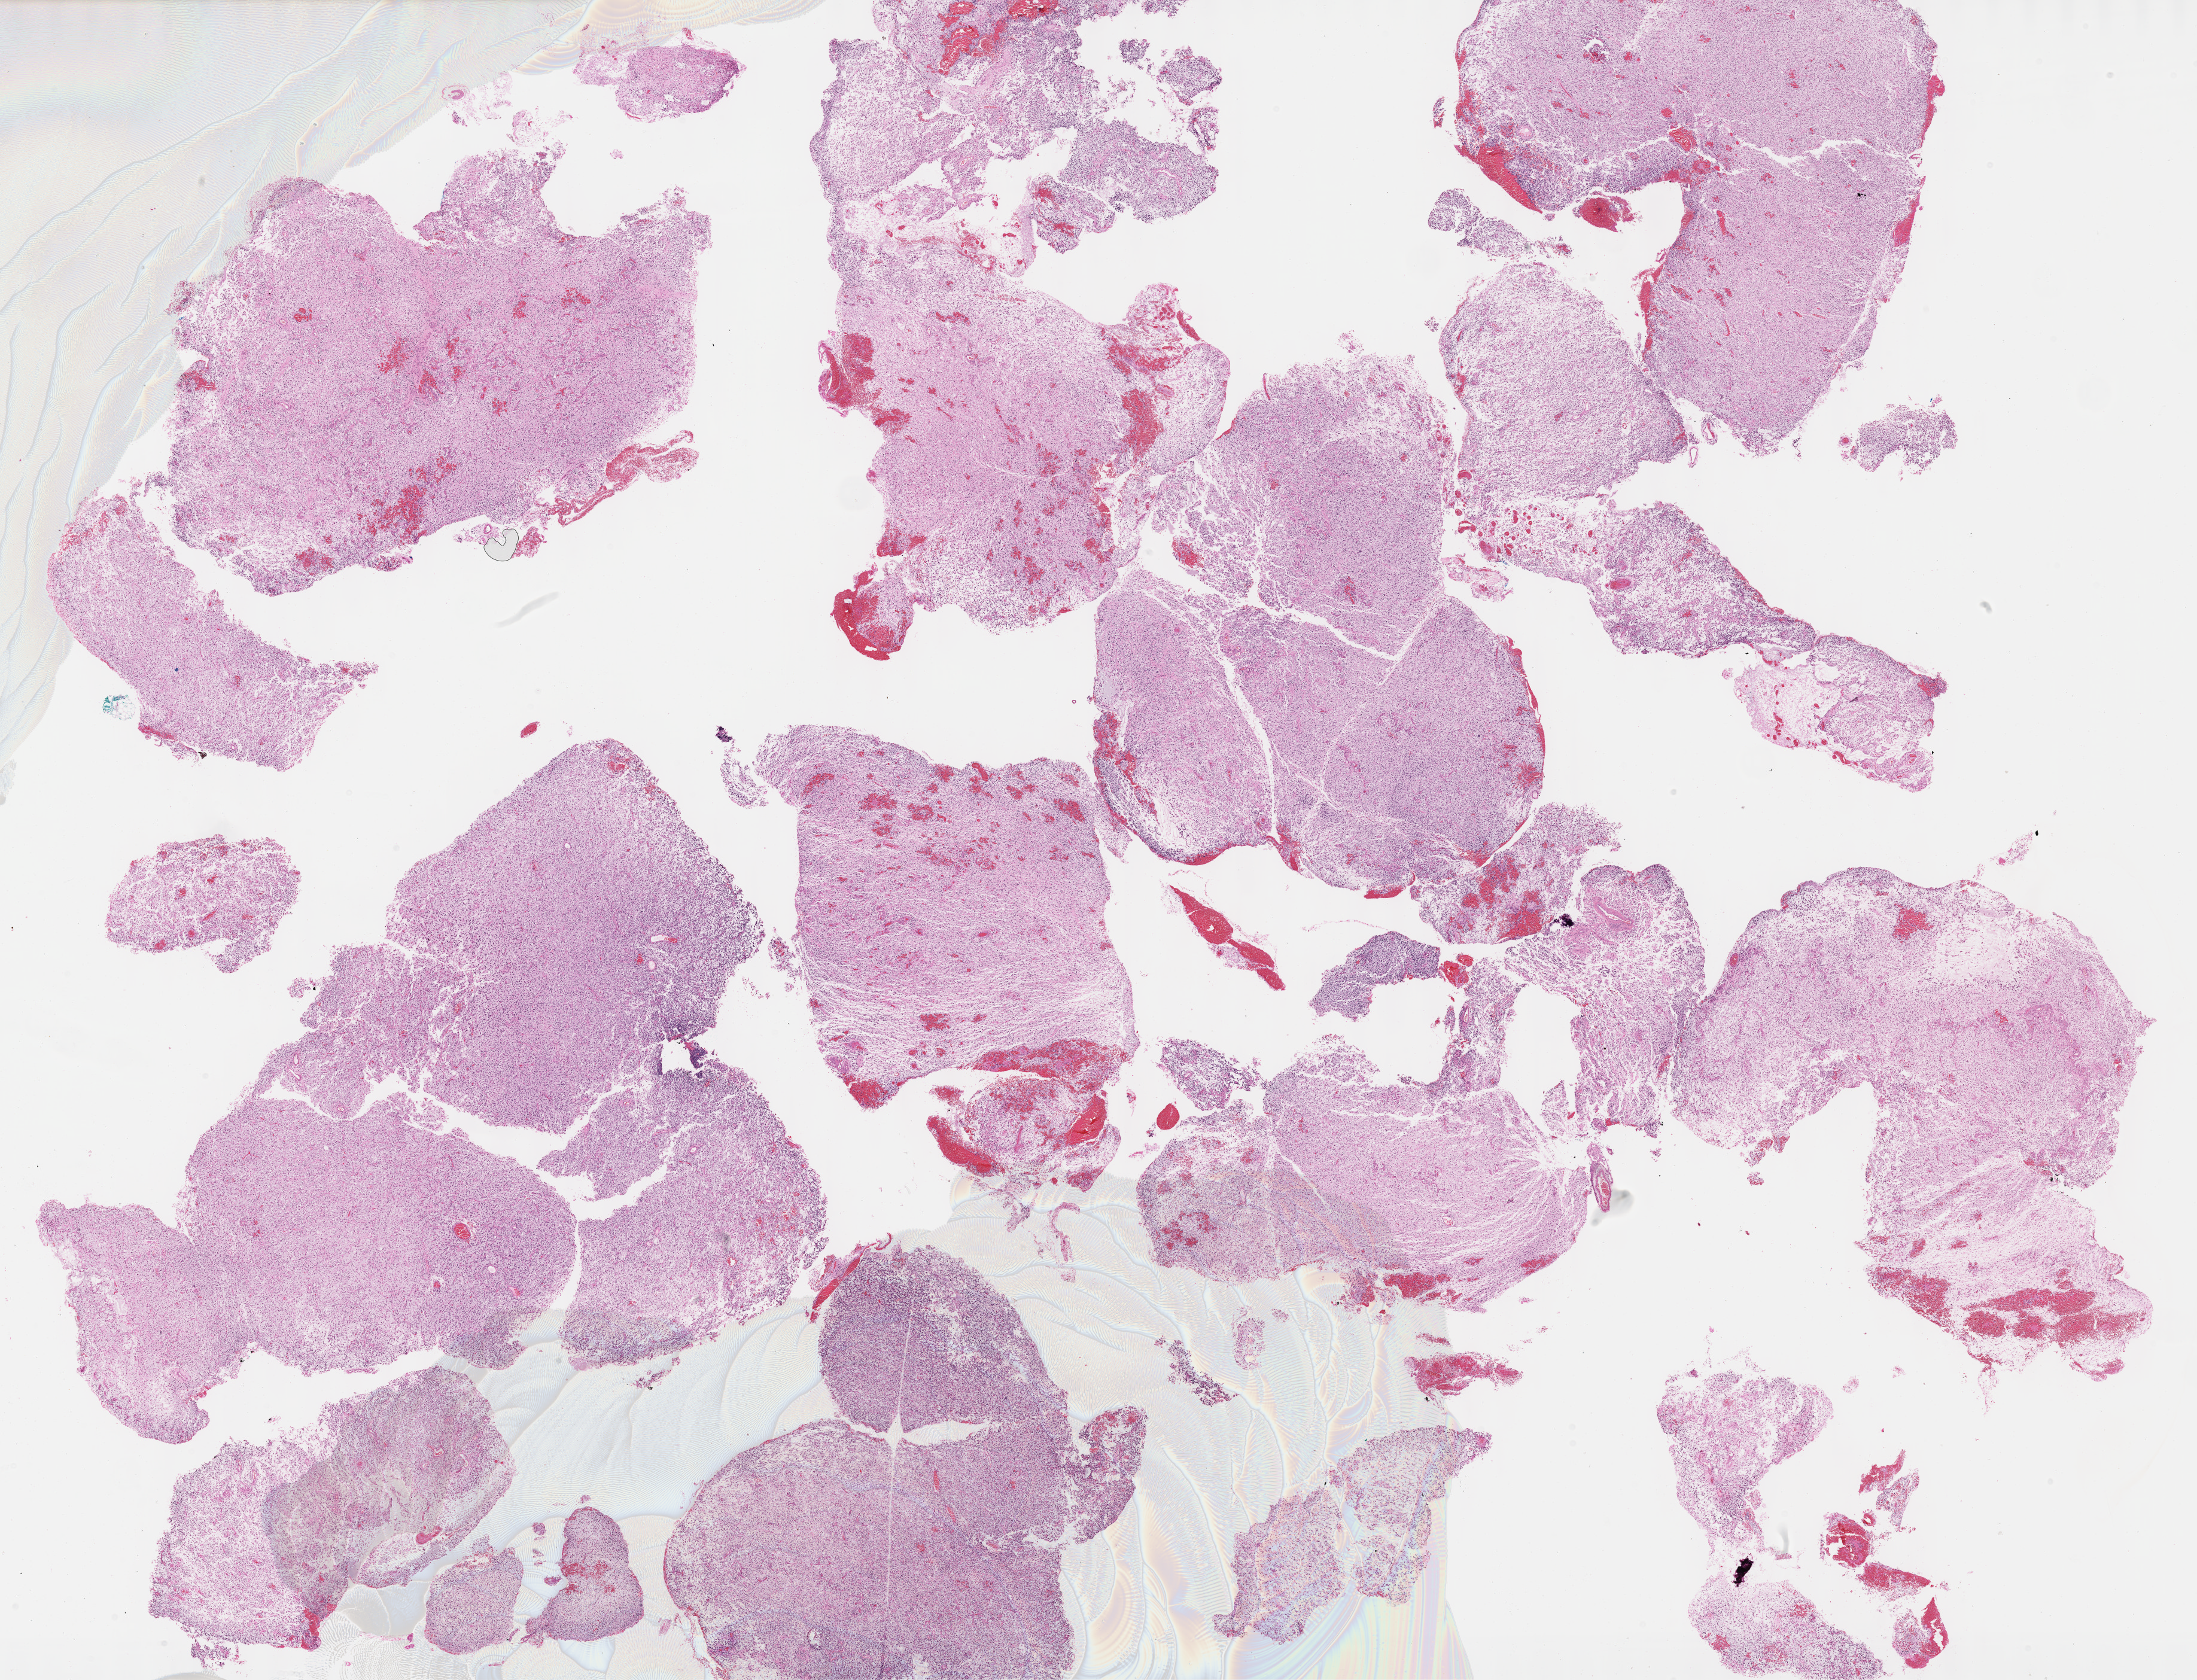
Digitized H&E tissue section (whole slide), whole scanned area (about 29.7 x 22.7 mm) shown as a low-resolution overview, formalin-fixed paraffin-embedded (FFPE) diagnostic section, sample: primary tumour, brain. Female patient; age at initial diagnosis 41 years. Histologic grade: G3 (poorly differentiated).
• histologic diagnosis: Mixed glioma (cerebrum)